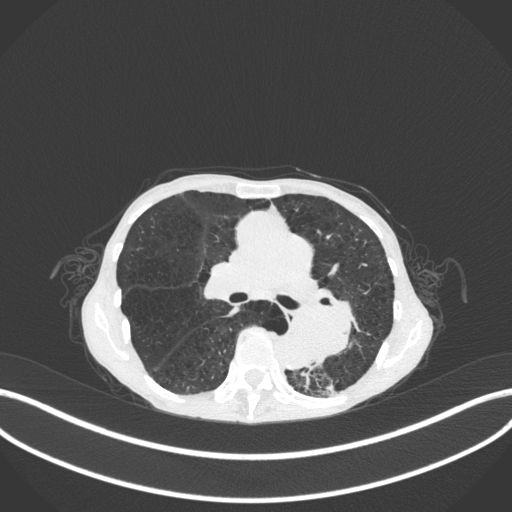
Chest CT, one axial slice; slice 163 of 347 in the series (ordered by position); lung window (W 1500 / L -600 HU); 1 mm slice thickness; 512 × 512 image matrix, field of view 400 × 400 mm. Female patient, age 70 years. Case-level facts recorded for this patient, not image findings: clinical TNM (as recorded): T3 N0 M0.
Structures marked on this image (bounding box drawn by a radiologist):
- lung tumour (recorded histology: small cell carcinoma): bounding box (x1, y1, x2, y2) in pixels: (301, 278, 362, 371)